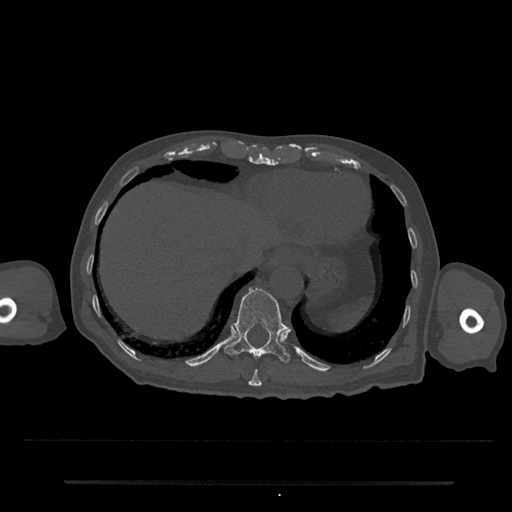
CT including the spine, one axial slice; position 263 of 797 along the scan axis; reconstruction kernel Br40s/3; bone window (W 1800 / L 400 HU); 0.5 mm slice thickness; 512 × 512 image matrix. Patient: male, 74 years. Case-level facts recorded for this patient, not image findings: primary cancer: prostate.
Outlined on this slice (semi-automatic segmentation, software-assisted and operator-edited):
- T10 vertebra: box from (x=248, y=369) to (x=262, y=387) px
- T11 vertebra: (x=224, y=287)–(x=291, y=363)